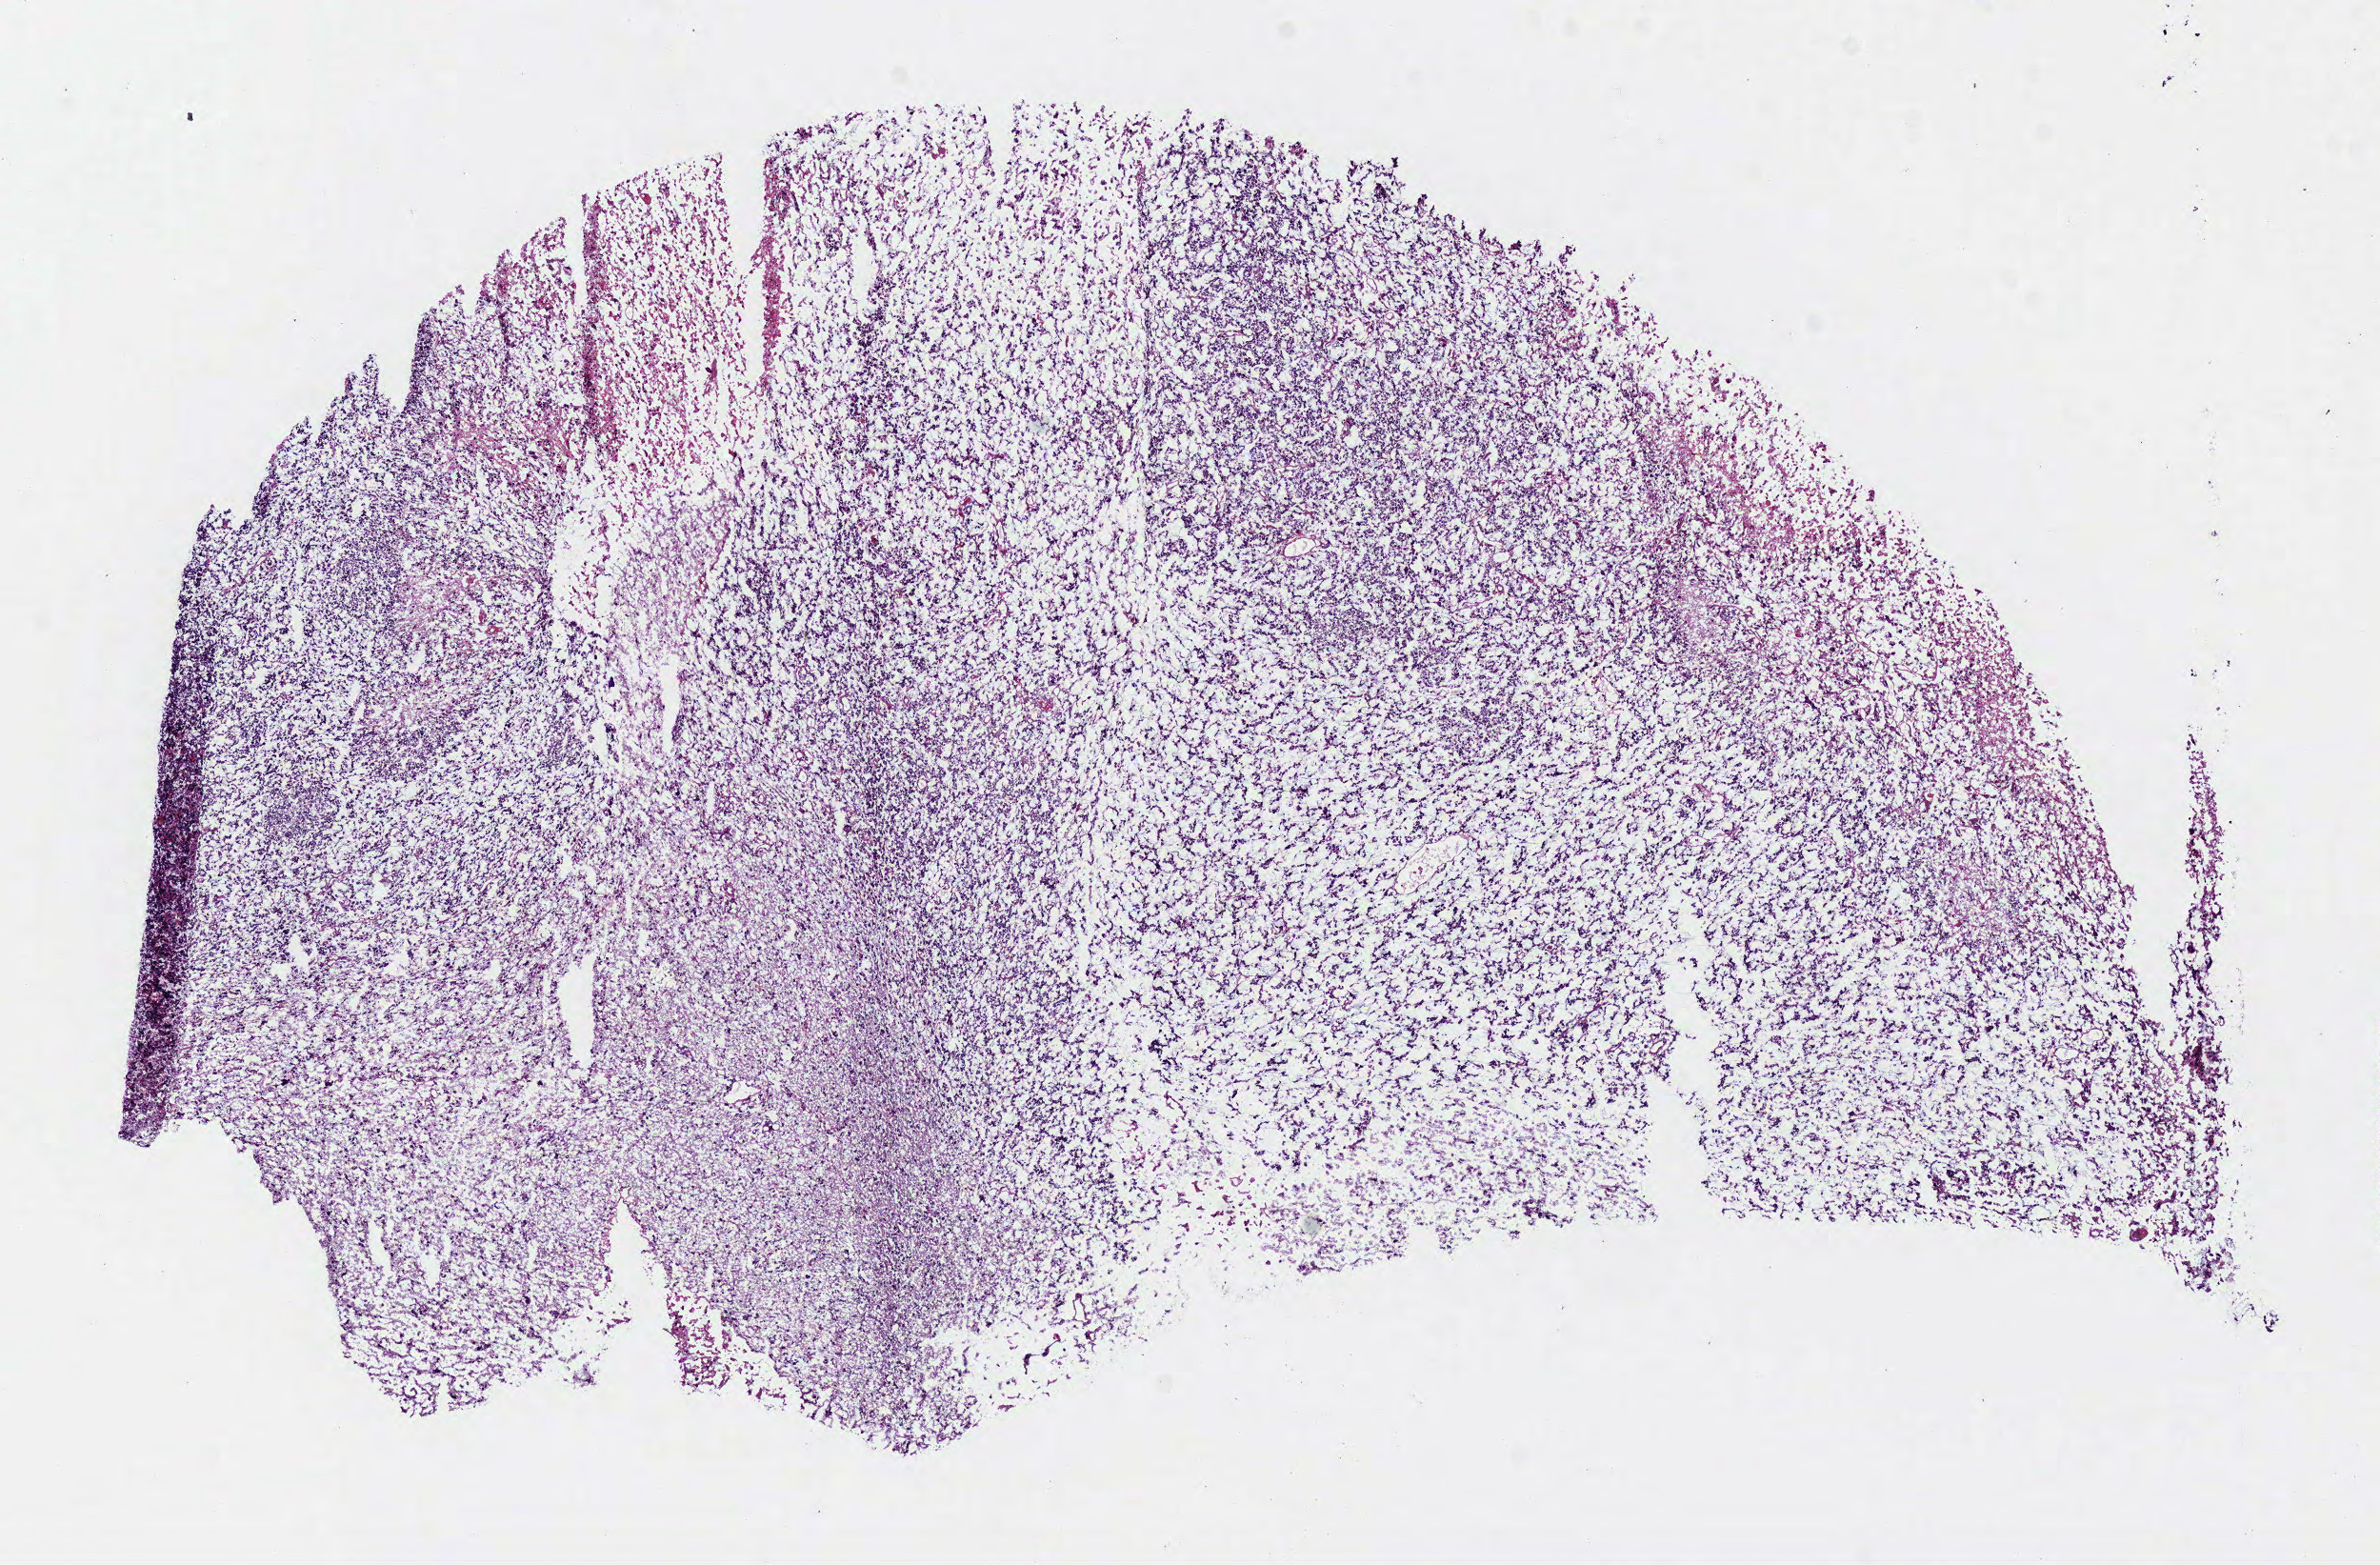
Whole-slide histology image, H&E-stained — shown as a low-resolution overview of the whole scanned area (about 9.8 x 6.5 mm); frozen section from the bottom of the tissue portion; sample: primary tumour, brain. Patient: female, age at initial diagnosis 53 years.
Pathologic diagnosis: Glioblastoma.